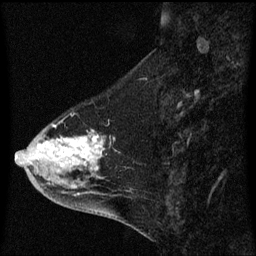
Breast MRI (dynamic contrast-enhanced), one sagittal slice; slice 22 of 60 in the series (ordered by position); dynamic contrast-enhanced series, image 2 of 3 at this slice position (ordered by acquisition); 1.5 T; TE 4.2 ms, TR 8.4 ms; 256 × 256 image matrix, field of view 200 × 200 mm. Patient: female, 46 years. From the clinical record (not read from this slice): setting: breast cancer imaged before/during neoadjuvant chemotherapy; receptor status: HER2-positive.
Outlined on this slice (semi-automatic segmentation, software-assisted and operator-edited):
- analysis volume of interest (the breast-tissue region the enhancement analysis was run in; not a lesion): box from (x=18, y=122) to (x=119, y=195) px
- tumour enhancement mask (voxels above the 70 % enhancement threshold inside the analysis volume of interest): (x=53, y=138)–(x=102, y=165)